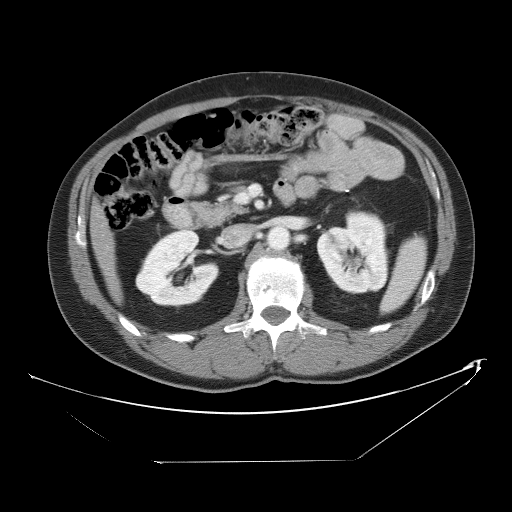
Contrast-enhanced abdominal CT, one axial slice. Slice 22 of 53 in the series (ordered by position). Reconstruction kernel STANDARD. 120 kVp. Intravenous contrast given. Soft-tissue window (W 400 / L 40 HU). 5 mm slice thickness. 512 × 512 image matrix, field of view 438 × 438 mm. Male patient, age 59 years. From the clinical record (not read from this slice): diagnosis: colorectal cancer liver metastases, imaged before liver resection; multiple liver metastases: yes; largest metastasis: 8.5 cm; disease in both lobes: no.
Annotated regions visible in this slice (outlined manually by an expert reader):
- liver: box from (x=92, y=208) to (x=118, y=298) px
- planned liver remnant (the part of the liver to remain after resection): (x=92, y=208)–(x=116, y=297)